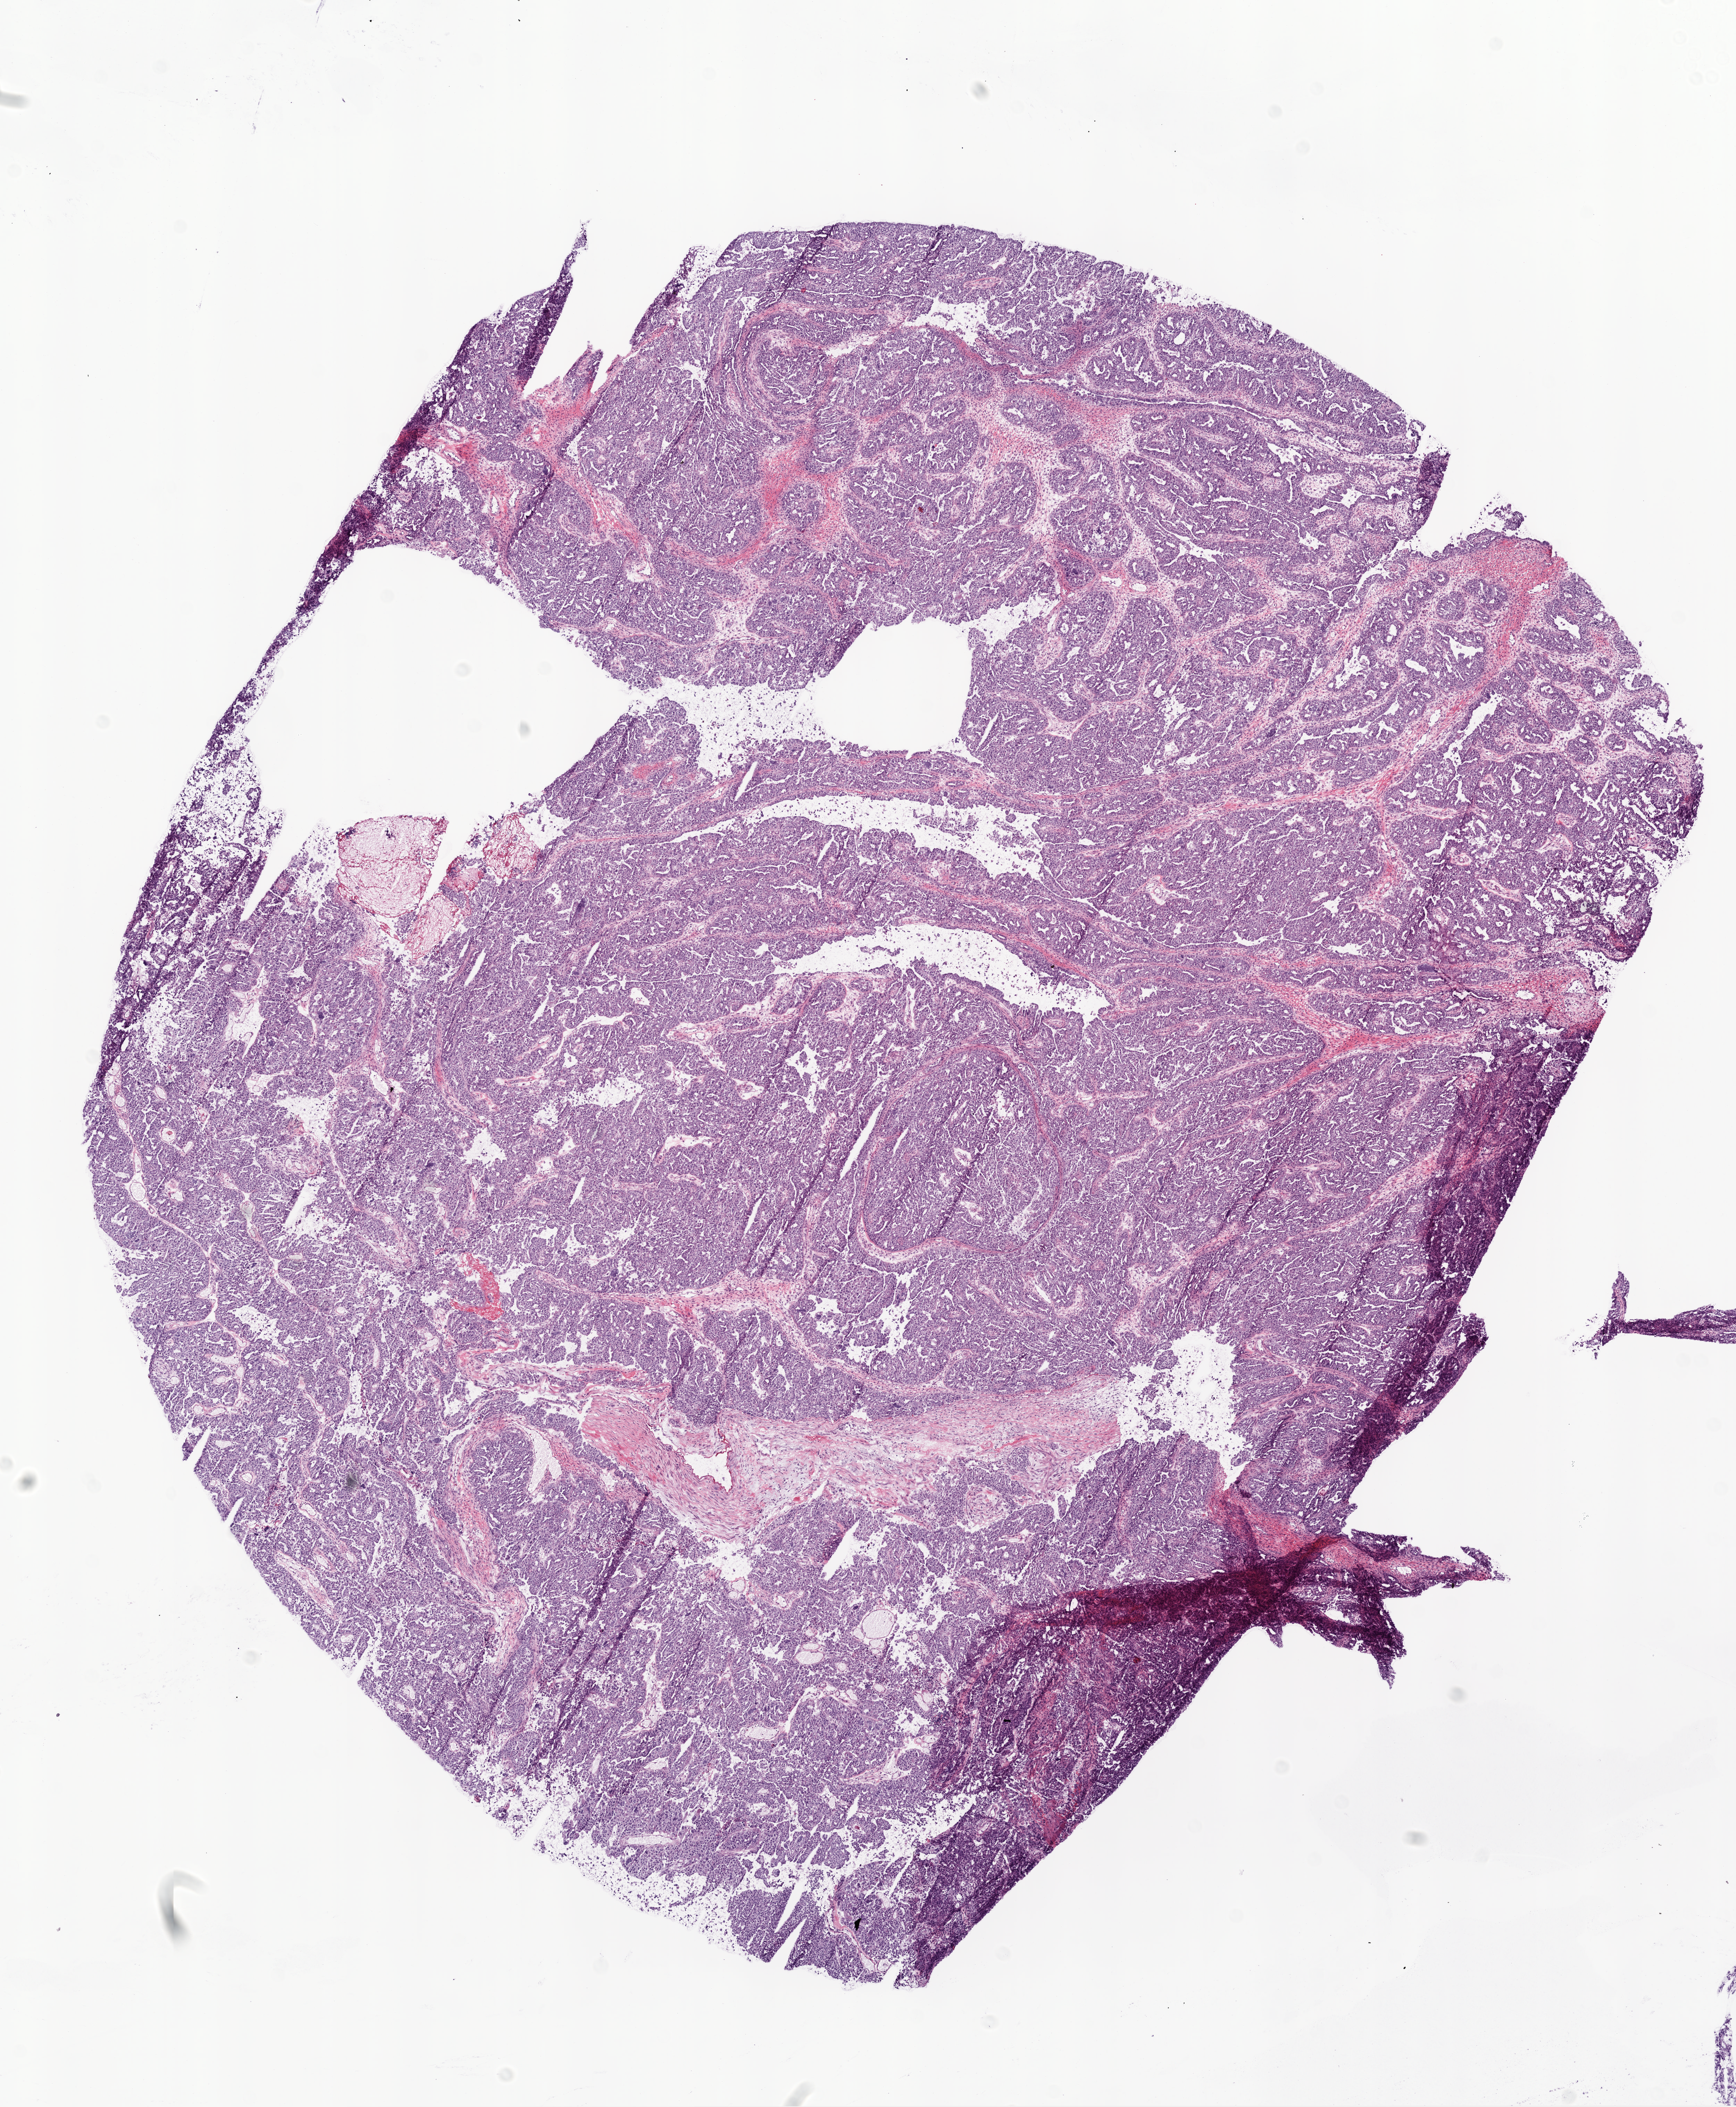
H&E-stained whole-slide image, whole scanned area (about 10.0 x 12.2 mm) shown as a low-resolution overview. Frozen section from the bottom of the tissue portion. Ovary, primary tumour sample. Female, age 49 years at initial diagnosis. Histologic grade: G3 (poorly differentiated). Slide review estimates, as recorded: tumour cells 94%, tumour nuclei 95%, normal cells 0%, stromal cells 5%, necrosis 1%.
Diagnosis: Serous cystadenocarcinoma, NOS. FIGO stage: IIIC. Laterality: bilateral.